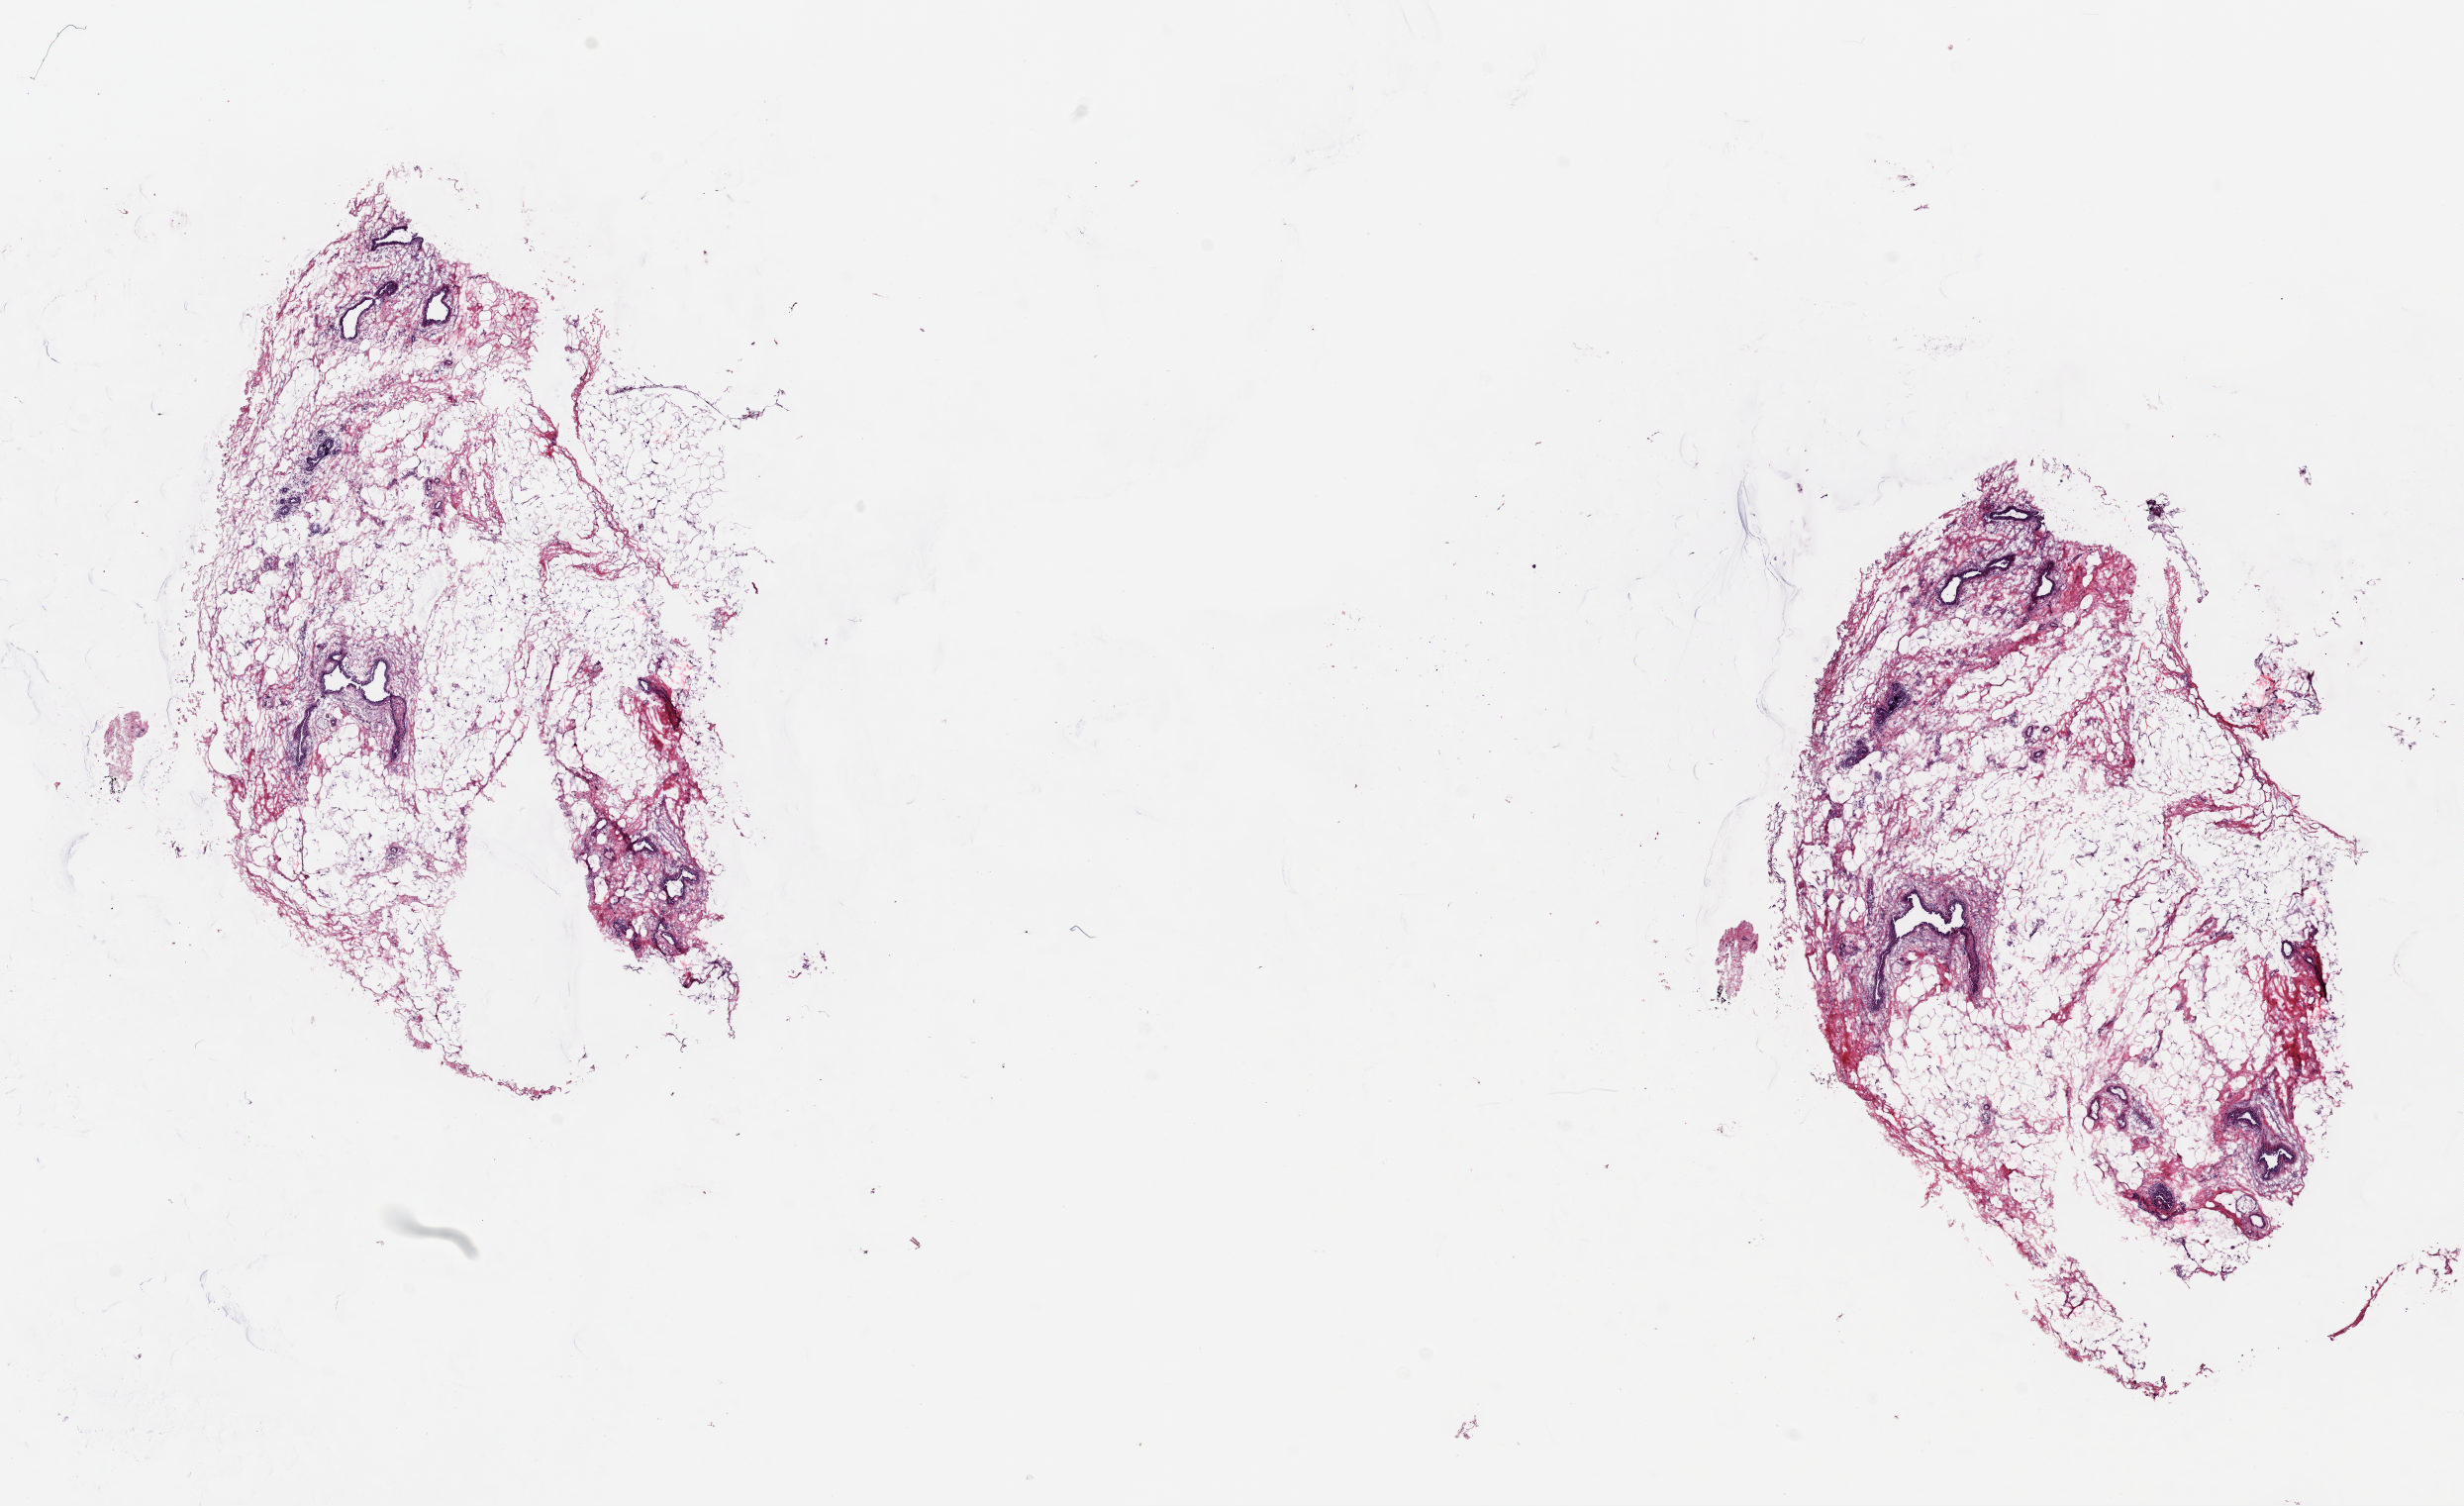
Hematoxylin and eosin (H&E) stained whole-slide image, a low-resolution overview of the entire scanned area, about 19.6 x 12.0 mm (from a 20x scan), frozen section, sample: solid tissue normal (non-tumour tissue), breast. Patient: female, age at initial diagnosis 87 years. Composition of this section per pathologist review: tumour cells 0%, tumour nuclei 0%, normal cells 5%, stromal cells 95%, necrosis 0%. Inflammatory infiltration, as recorded: lymphocyte infiltration 0%, monocyte infiltration 0%, neutrophil infiltration 0%.
This section: solid tissue normal sample (biorepository sample class). Patient diagnosis: Lobular carcinoma, NOS.